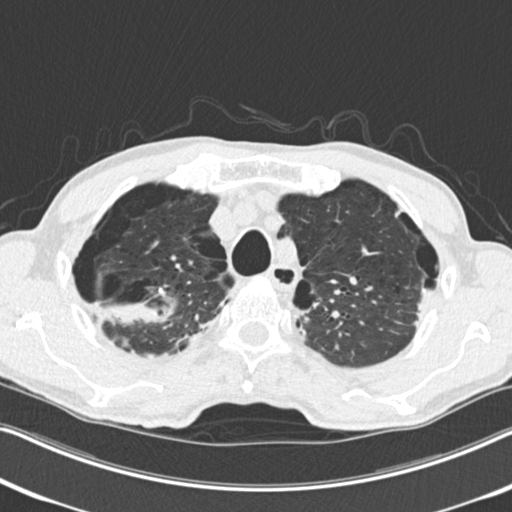
Low-dose screening chest CT, one axial slice. Reconstruction kernel B30f. Lung window (W 1500 / L -600 HU). 2 mm slice thickness. 512 × 512 image matrix, field of view 334 × 334 mm.
Annotated regions visible in this slice (outlined manually by an expert reader):
- lesion 1 (tumor, upper lobe of right lung): bounding box <94,303,159,323> (left, top, right, bottom; pixels)